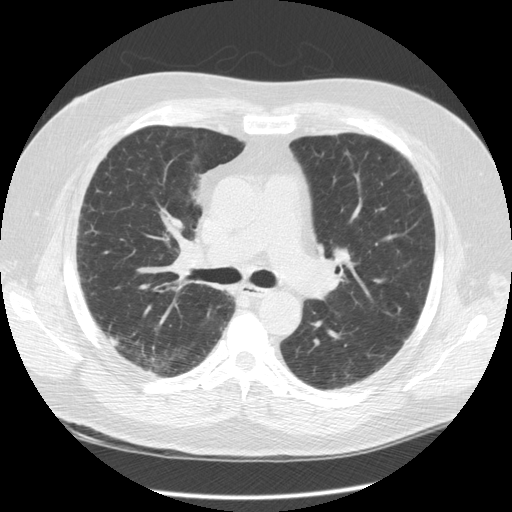
Chest CT (low-dose screening protocol), one axial image, second annual screen, lung window (W 1500 / L -600 HU), 2.5 mm slice thickness, 120 kVp. Male, age 56 years at enrolment. Current smoker at enrolment.
• Lesion marked by an expert reader, bounding box (x1, y1, x2, y2) in pixels: (99, 322, 135, 359).
• Screening reader's record for this exam (one nodule recorded; not confirmed to be the boxed lesion): non-calcified nodule or mass ≥4 mm, right upper lobe, 7 × 5 mm, poorly defined margins, soft tissue attenuation, pre-existing on the prior screen: no.
• Later outcome: lung cancer diagnosed 399 days after this screen (after the third annual screen) — large cell neuroendocrine carcinoma, right upper lobe, stage IIIA (AJCC 6th edition), 10 mm at pathology.